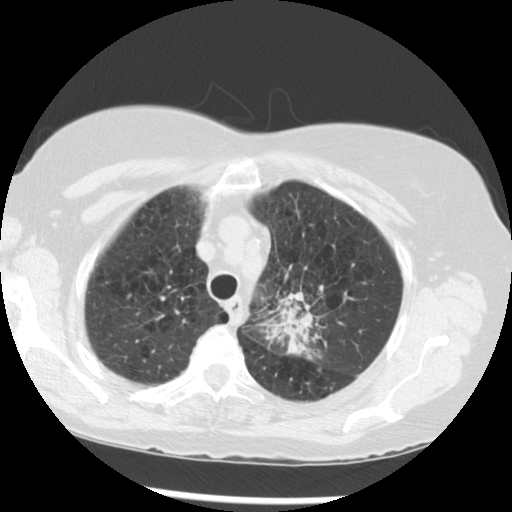
Low-dose screening chest CT, one axial slice; position 226 of 283 along the scan axis; reconstruction kernel STANDARD; lung window (W 1500 / L -600 HU); 2.5 mm slice thickness; 512 × 512 image matrix, field of view 330 × 330 mm.
Structures marked on this image (expert manual segmentation):
- lesion 1 (tumor, upper lobe of left lung): bounding box [x1, y1, x2, y2] px = [271, 291, 319, 361]